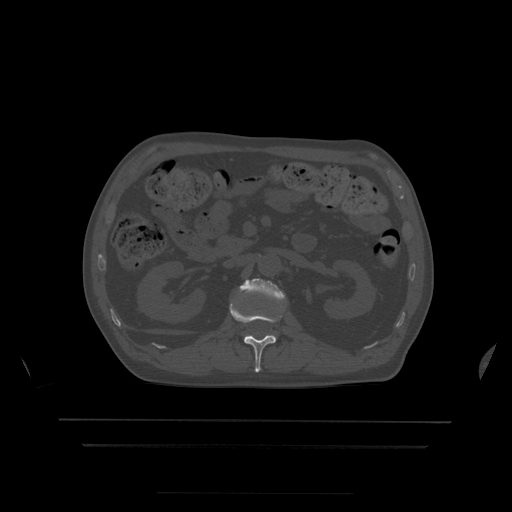
CT including the spine, one axial slice. Slice 162 of 522 in the series (ordered by position). Bone window (W 1800 / L 400 HU). 1.25 mm slice thickness. 512 × 512 image matrix, field of view 436 × 436 mm. Patient age 68 years. From the clinical record (not read from this slice): primary cancer: urothelial.
Structures marked on this image (semi-automatically segmented with operator editing):
- L1 vertebra: bounding box <230,303,281,373> (left, top, right, bottom; pixels)
- L2 vertebra: <240,279,285,302>